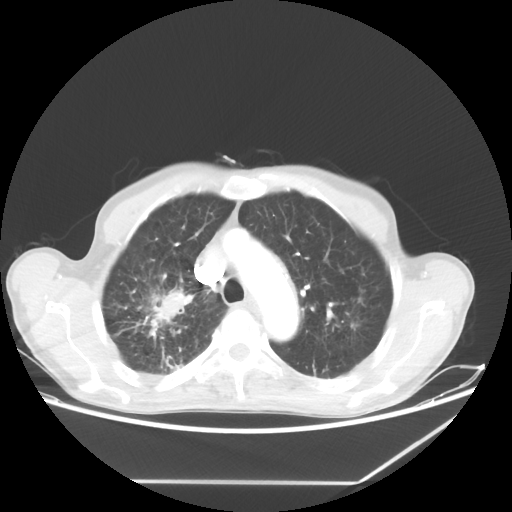
Chest CT, one axial slice; position 48 of 65 along the scan axis; 80 kVp; lung window (W 1500 / L -600 HU); 5 mm slice thickness; 512 × 512 image matrix, field of view 397 × 397 mm. Male patient, age 68 years. Case-level facts recorded for this patient, not image findings: clinical TNM (as recorded): T3 N3 M0.
Outlined on this slice (rectangle marked by the reading radiologist):
- lung tumour (recorded histology: adenocarcinoma): box from (x=135, y=279) to (x=189, y=338) px